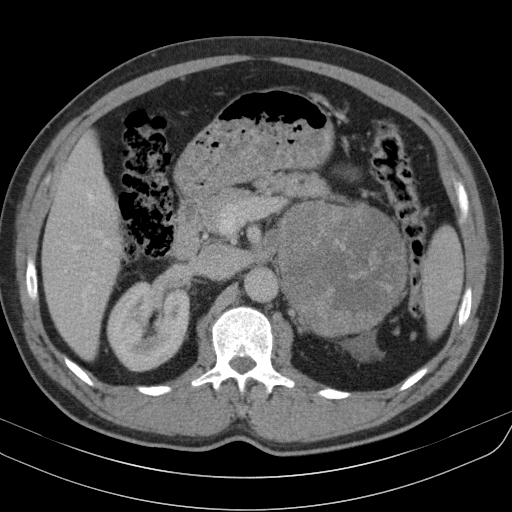
Contrast-enhanced abdominal CT, one axial slice; slice 65 of 91 in the series (ordered by position); reconstruction kernel B31s; intravenous contrast given; soft-tissue window (W 400 / L 40 HU); 512 × 512 image matrix. Male patient, age 51 years. Case-level facts recorded for this patient, not image findings: diagnosis: adrenocortical carcinoma; tumour side: left adrenal; tumour size at pathology: 18 cm; Ki-67 index: 40 %; stage (as recorded): 3.
Outlined on this slice (semi-automatic segmentation, software-assisted and operator-edited):
- mass: bounding box (x1, y1, x2, y2) in pixels: (280, 201, 407, 334)